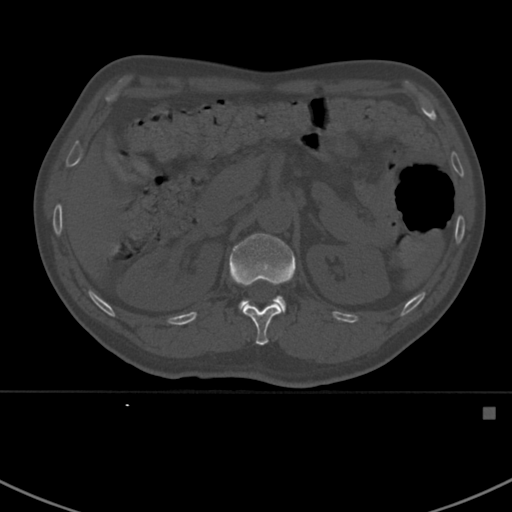
CT including the spine, one axial slice; slice 320 of 412 in the series (ordered by position); reconstruction kernel Br40s; 120 kVp; bone window (W 1800 / L 400 HU); 512 × 512 image matrix, field of view 358 × 358 mm. Patient: male, 59 years. From the clinical record (not read from this slice): primary cancer: prostate.
Annotated regions visible in this slice (semi-automatic segmentation, software-assisted and operator-edited):
- L1 vertebra: bounding box [x1, y1, x2, y2] px = [229, 233, 296, 313]
- T12 vertebra: [242, 303, 281, 346]